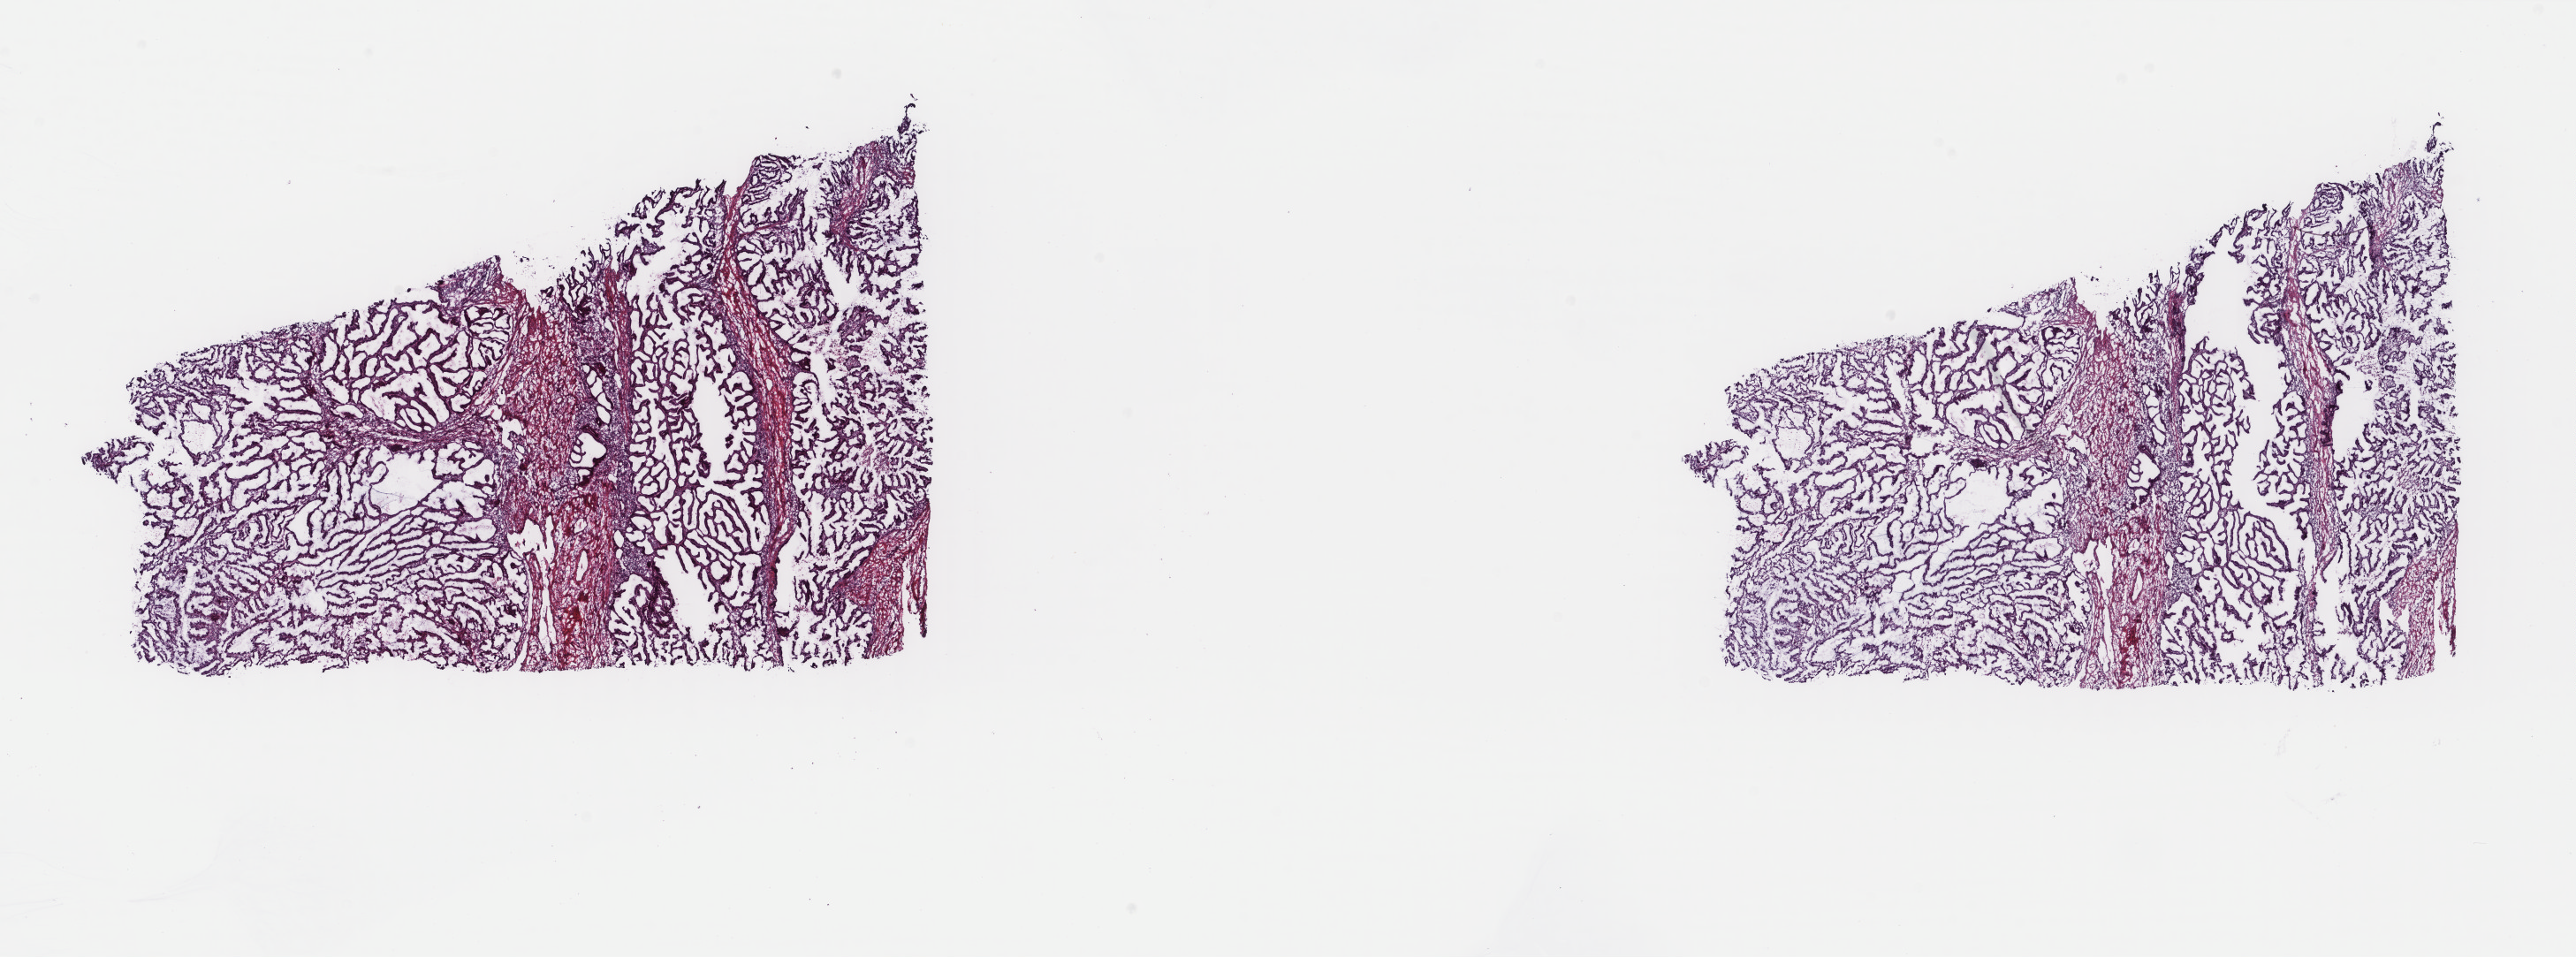
H&E whole-slide image — whole scanned area (about 23.1 x 8.6 mm) shown as a low-resolution overview; frozen section; primary tumour sample from the uterus. Patient: female, age at initial diagnosis 57 years. Histologic grade: G3 (poorly differentiated). Slide review estimates, as recorded: tumour cells 85%, tumour nuclei 85%, normal cells 0%, stromal cells 15%, necrosis 0%. Inflammatory infiltration, as recorded: lymphocyte infiltration 10%, monocyte infiltration 3%, neutrophil infiltration 3%.
Lymph nodes positive (case pathology): 0 of 15 examined. FIGO stage: II. Histologic diagnosis: Endometrioid adenocarcinoma, NOS (endometrium).